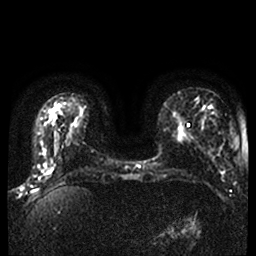
Breast MRI, one axial slice; slice 12 of 42 in the series (ordered by position); diffusion-weighted series; image 2 of 4 stored at this slice position (different b-values; order by instance number); 1.5 T; 4 mm slice thickness; 256 × 256 image matrix, field of view 340 × 340 mm. Female patient.
Outlined on this slice (outlined manually by an expert reader):
- tumour on diffusion-weighted imaging: bounding box <45,169,53,179> (left, top, right, bottom; pixels)